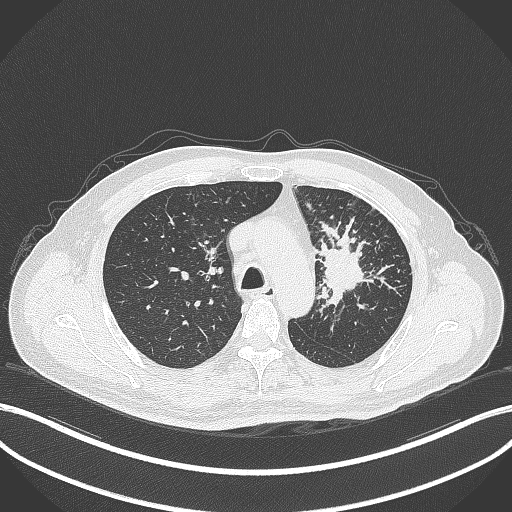
Chest CT, one axial slice; position 254 of 386 along the scan axis; lung window (W 1500 / L -600 HU); 1 mm slice thickness; 512 × 512 image matrix. Patient: male, 69 years. Case-level facts recorded for this patient, not image findings: clinical TNM (as recorded): T2a N2 M0.
Annotated regions visible in this slice (rectangle marked by the reading radiologist):
- lung tumour (recorded histology: adenocarcinoma): bounding box [x1, y1, x2, y2] px = [312, 230, 365, 312]